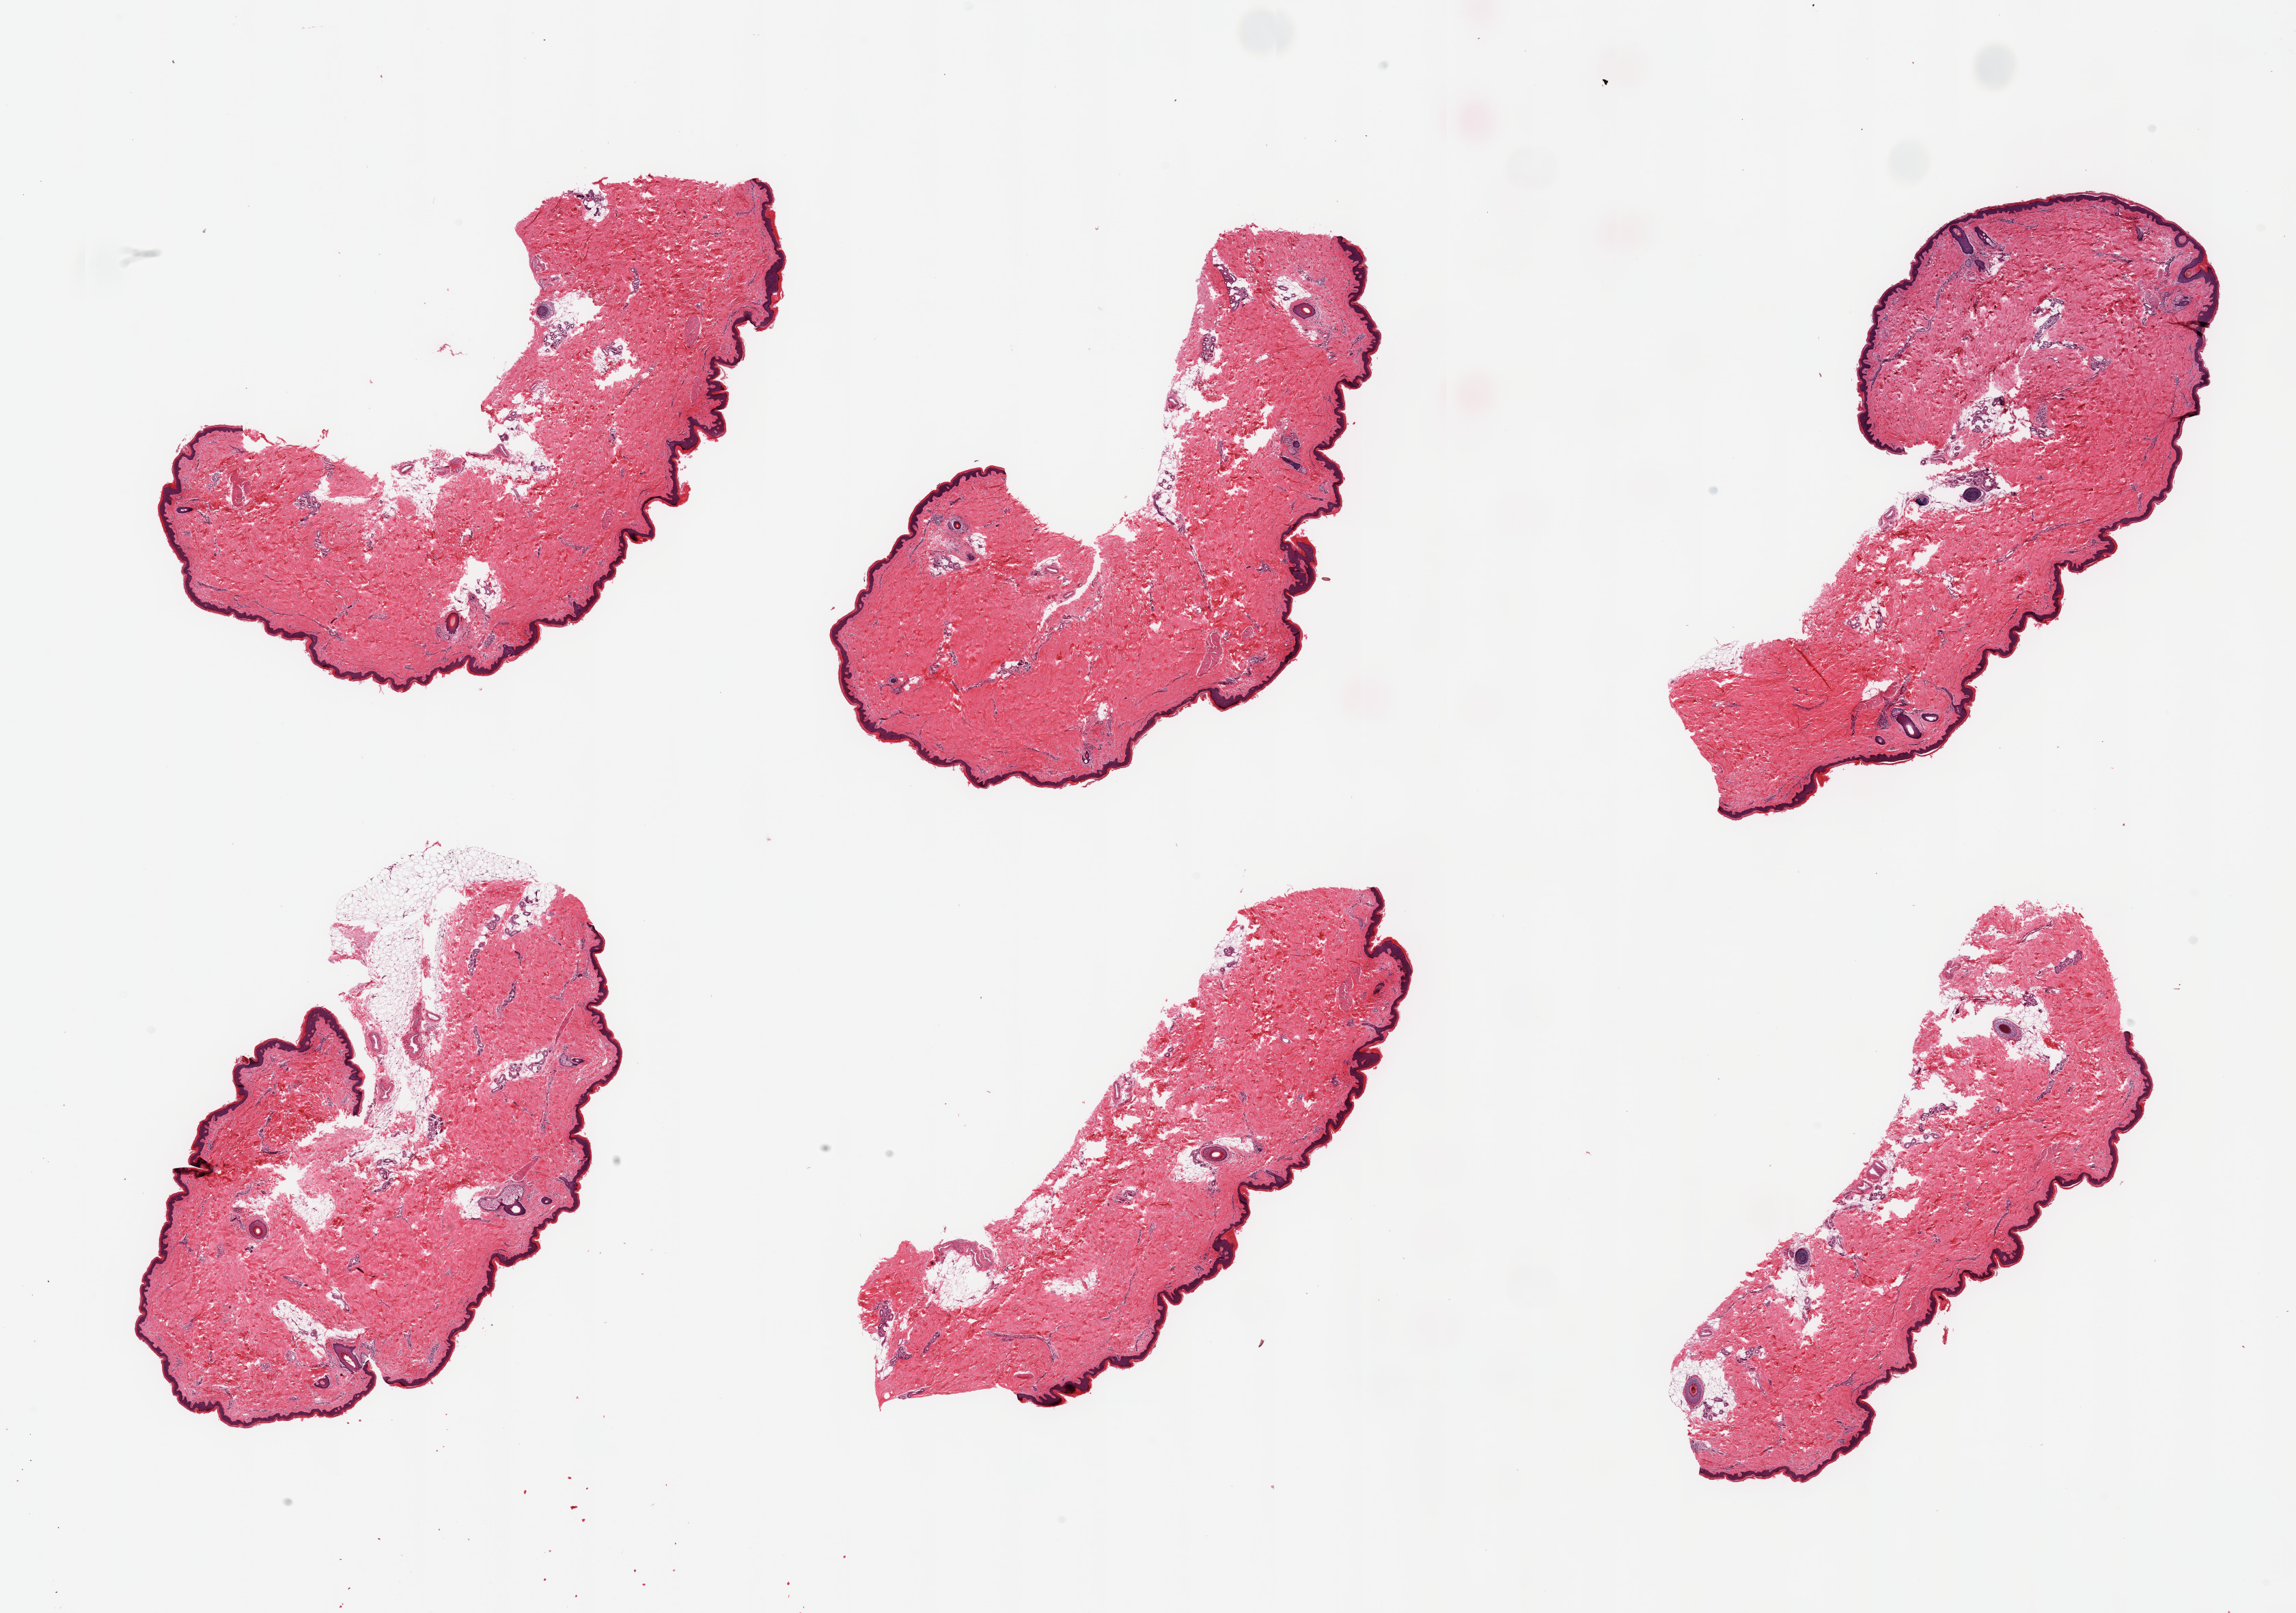
Whole-slide image, hematoxylin and eosin (H&E) stain — low-resolution overview of the scanned area, about 26.6 x 18.7 mm (acquisition: 20x scan), PAXgene-fixed, paraffin-embedded tissue, section of skin of lower leg (target tissue), donor tissue sample. Male donor.
Review note (as recorded): 6 pieces, trace dermal fat; squamous epithelium is ~0 microns.